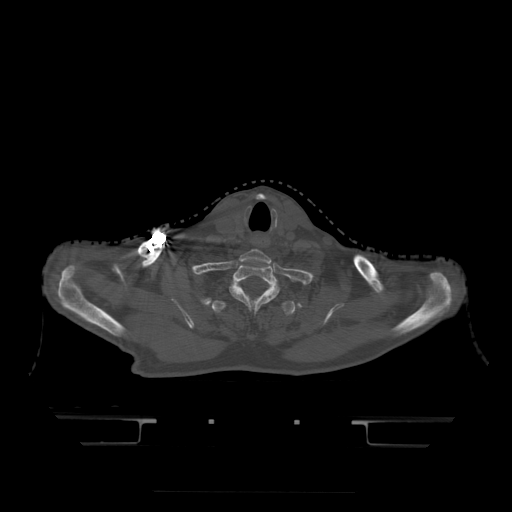
CT including the spine, one axial slice. Position 397 of 522 along the scan axis. Bone window (W 1800 / L 400 HU). 512 × 512 image matrix, field of view 436 × 436 mm. Patient age 68 years. Case-level facts recorded for this patient, not image findings: primary cancer: urothelial.
Annotated regions visible in this slice (semi-automatically segmented with operator editing):
- T1 vertebra: bounding box <230,264,279,309> (left, top, right, bottom; pixels)
- T2 vertebra: <212,300,296,317>